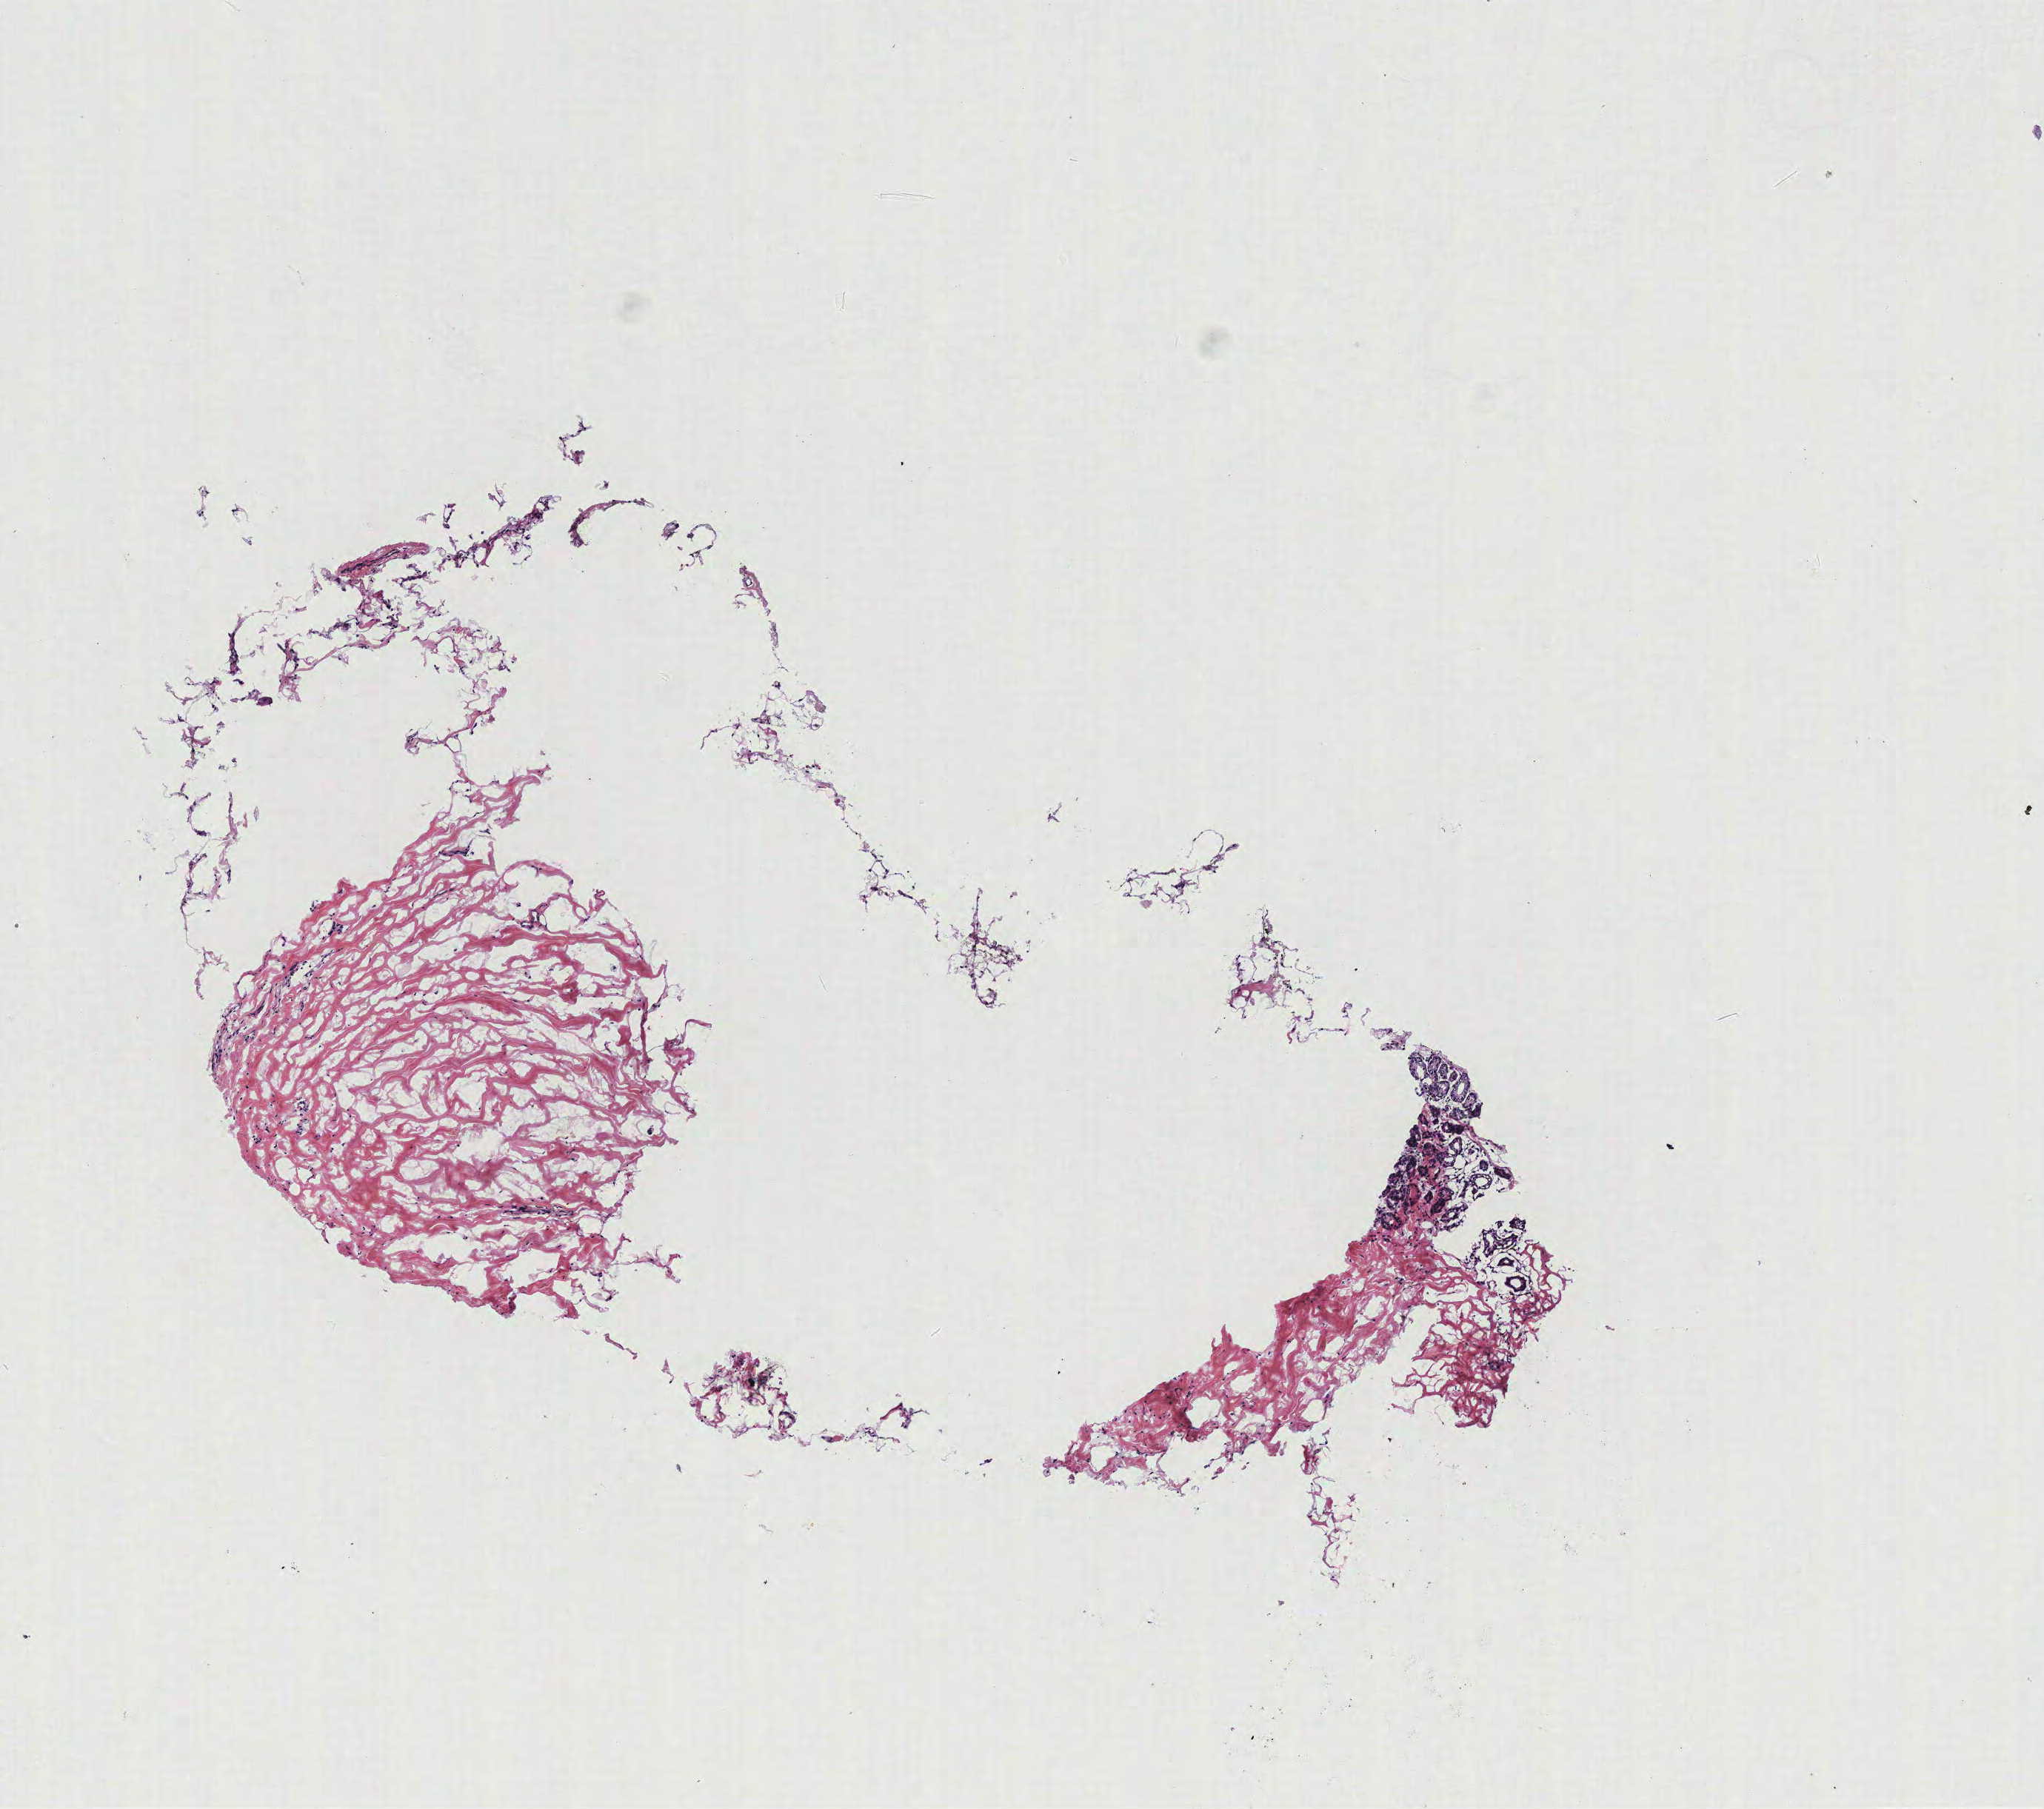
H&E whole-slide image, low-resolution overview of the scanned area, about 5.5 x 4.9 mm; breast, tissue type not recorded. Female, 46 y/o.
Patient diagnosis: Infiltrating duct carcinoma, NOS.